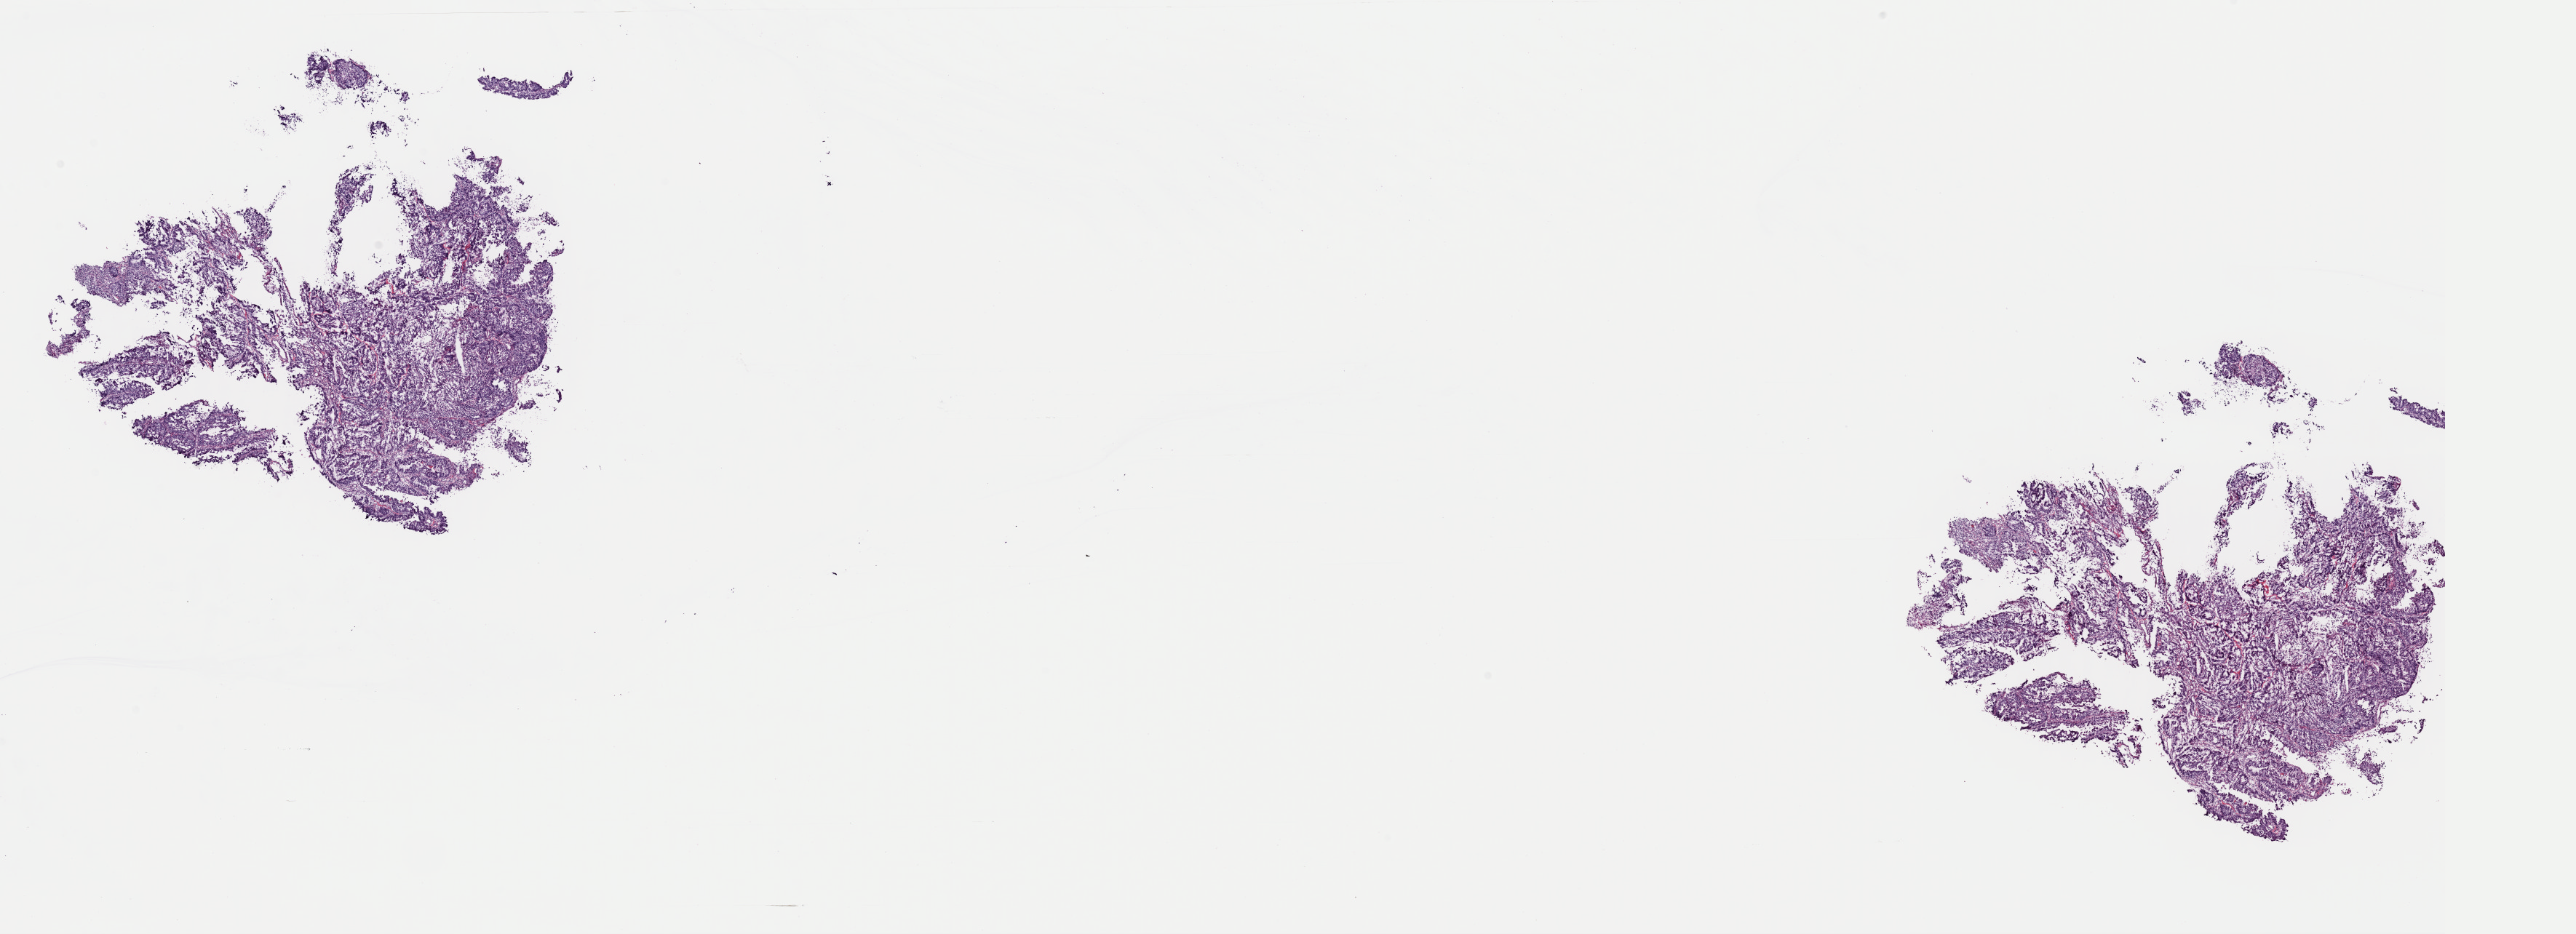
Whole-slide histology image, H&E — whole scanned area (about 28.0 x 10.1 mm) shown as a low-resolution overview. Frozen section. Uterus, primary tumour sample. Patient: female, age at initial diagnosis 87 years. Histologic grade: G3 (poorly differentiated). Composition of this section per pathologist review: tumour cells 80%, tumour nuclei 80%, normal cells 0%, stromal cells 10%, necrosis 10%. Infiltration values recorded for this section: lymphocyte infiltration 40%, monocyte infiltration 20%, neutrophil infiltration 20%.
FIGO stage: II. Pathologic diagnosis: Endometrioid adenocarcinoma, NOS (endometrium).